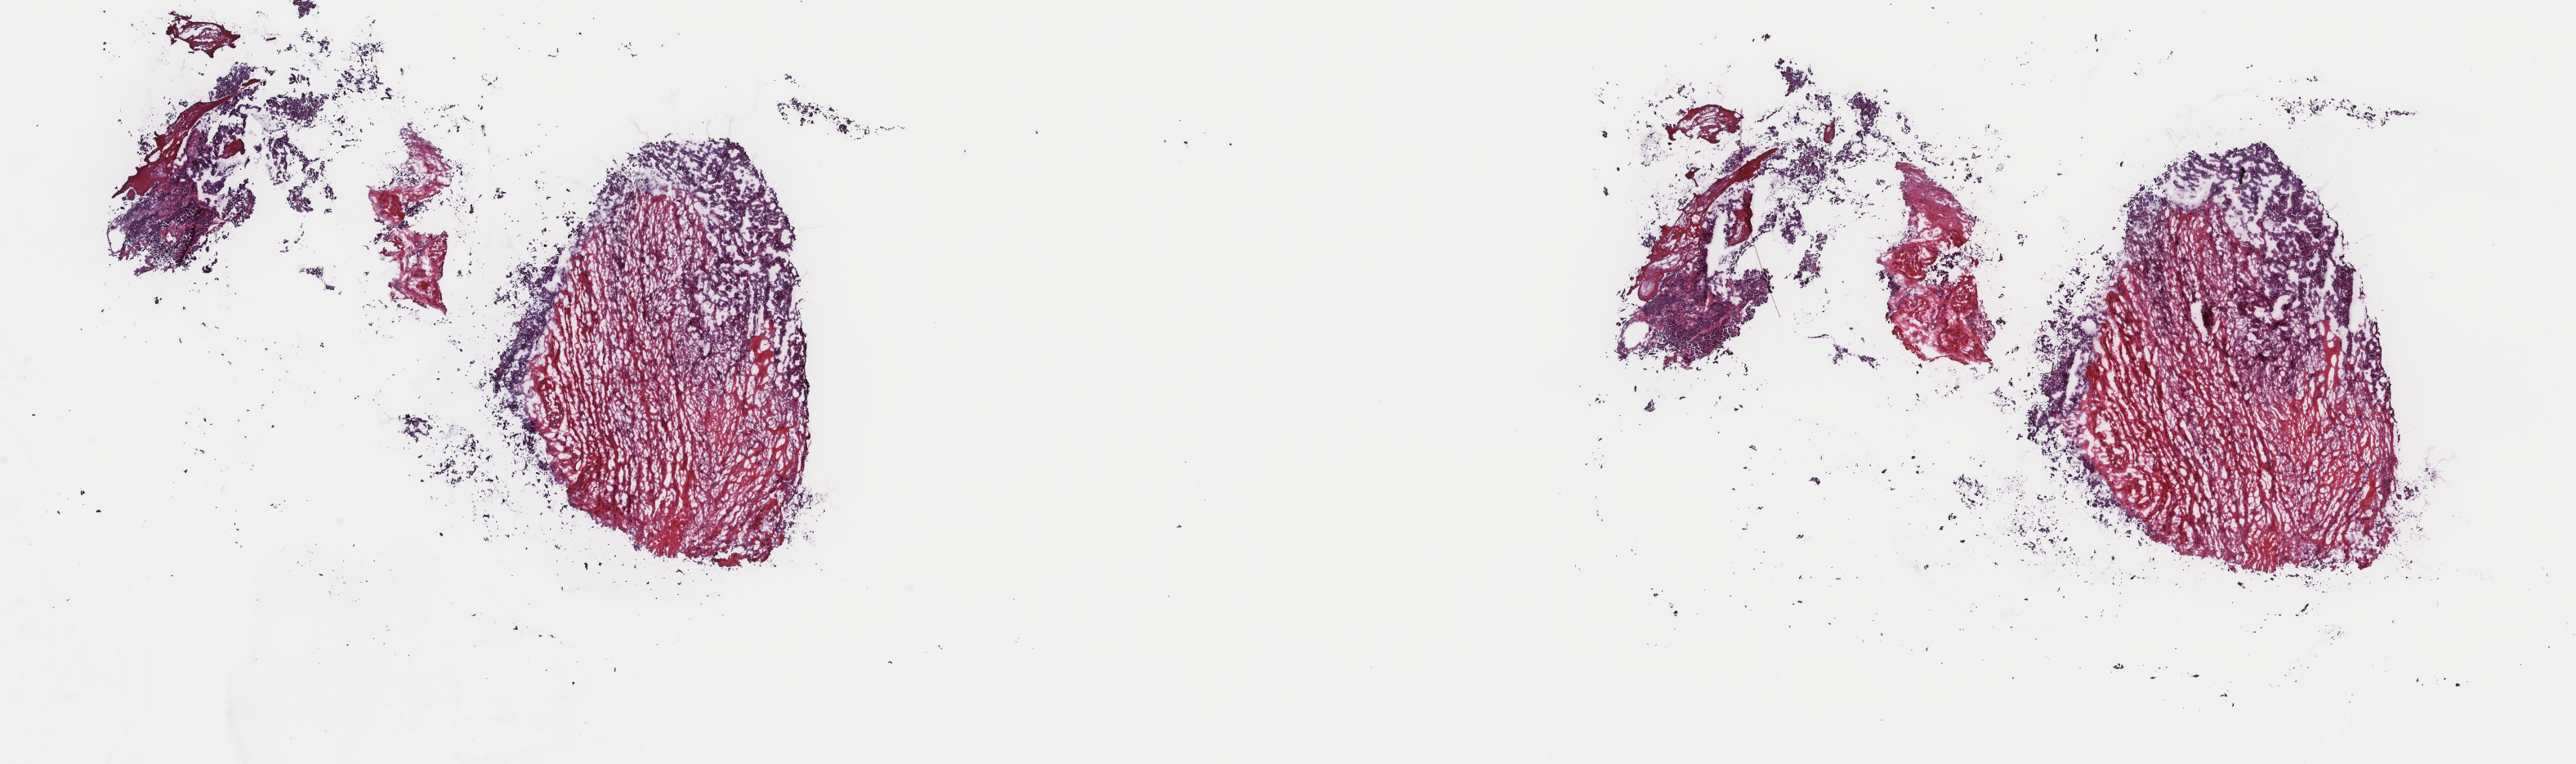
Digitized H&E tissue section (whole slide) — whole scanned area (about 25.0 x 7.4 mm) shown as a low-resolution overview; frozen section; thyroid, primary tumour sample. Male patient; age at initial diagnosis 70 years. Slide review estimates, as recorded: tumour cells 40%, tumour nuclei 100%, normal cells 0%, stromal cells 60%, necrosis 0%. Inflammatory infiltration, as recorded: lymphocyte infiltration 0%, monocyte infiltration 0%, neutrophil infiltration 1%.
Pathologic diagnosis: Papillary adenocarcinoma, NOS. Laterality: right. AJCC pathologic stage: III (6th edition).